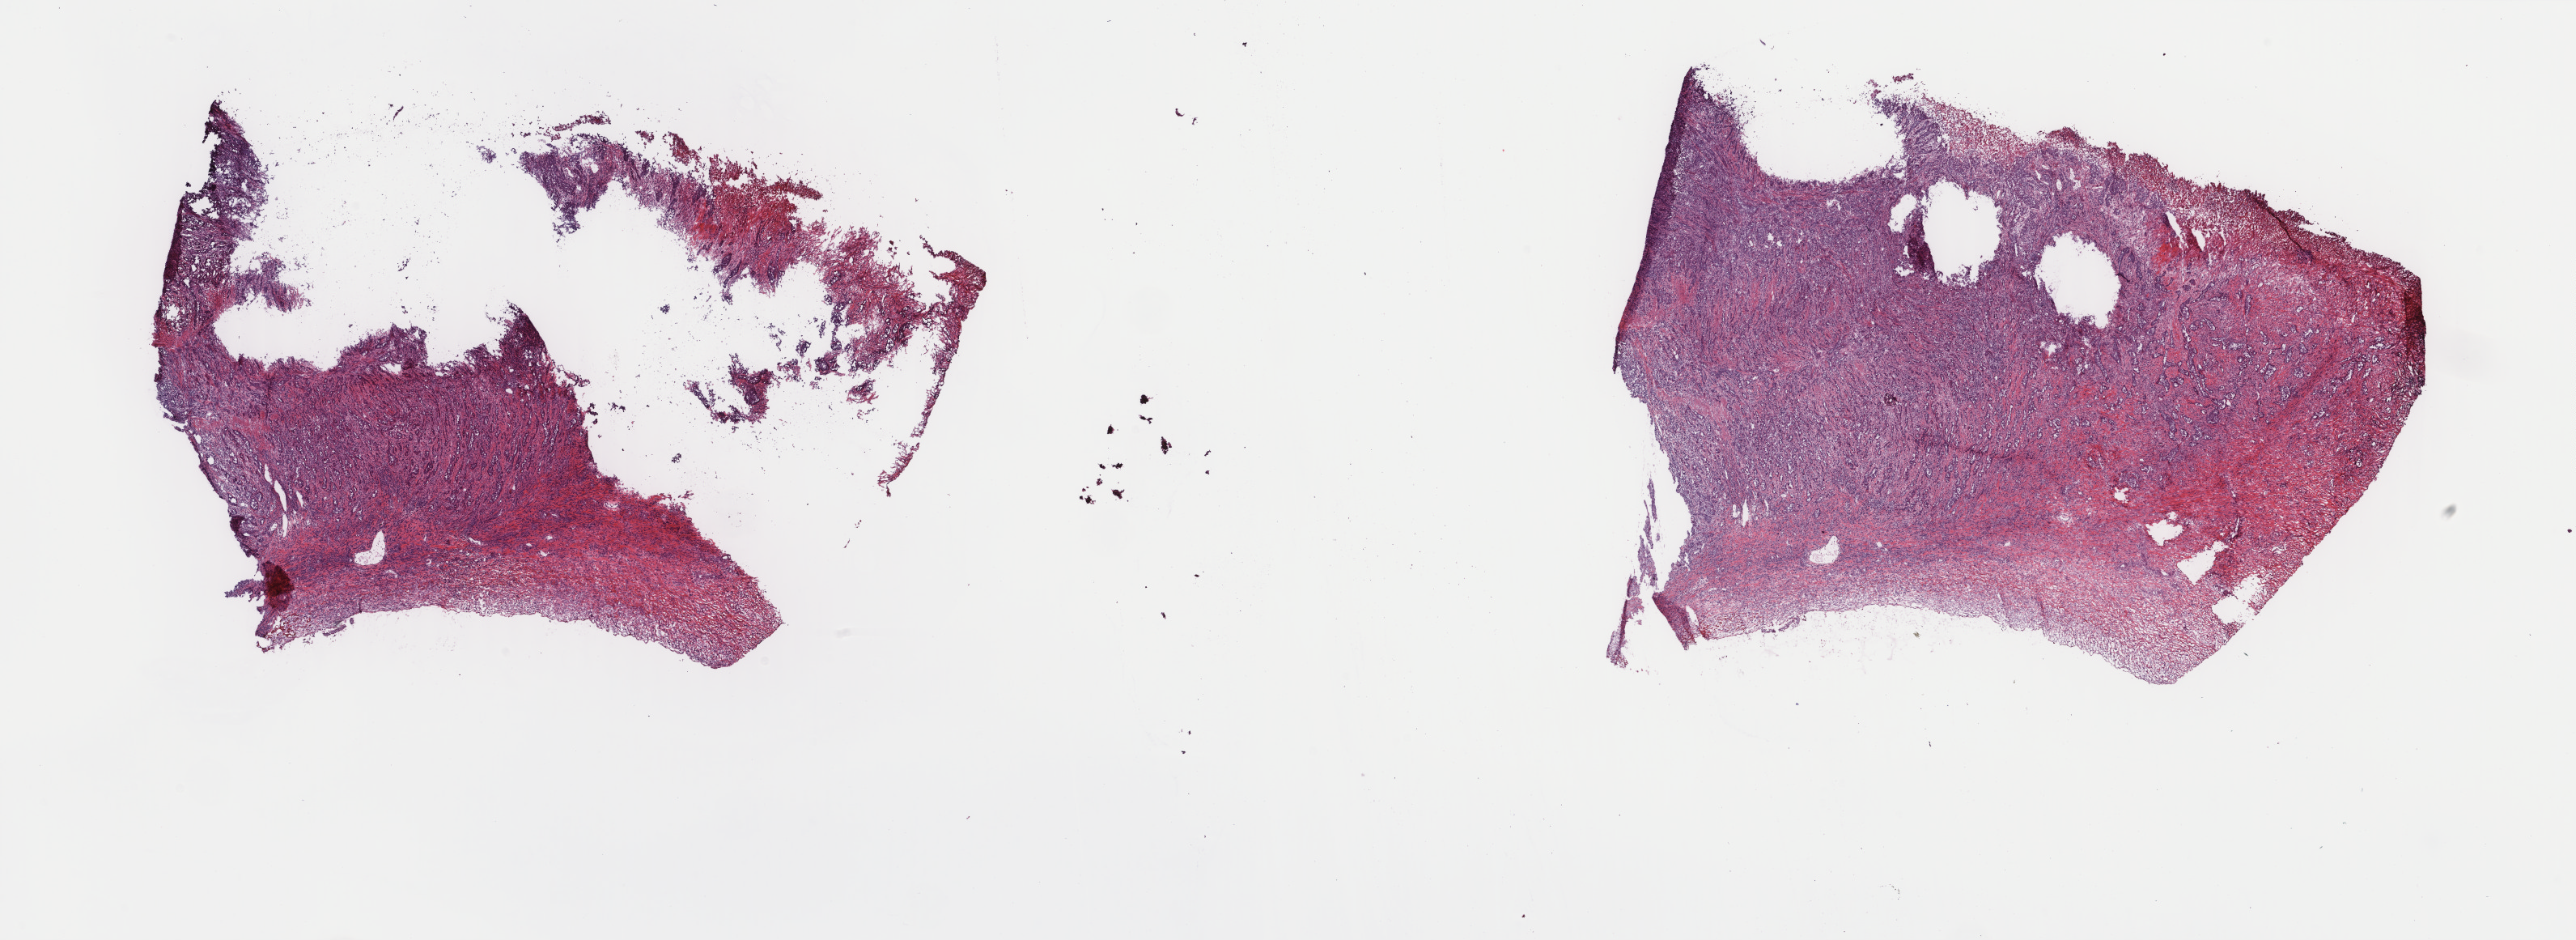
Whole-slide histology image, H&E, low-resolution overview of the scanned area, about 25.3 x 9.2 mm (from a 40x scan); frozen section from the top of the tissue portion; stomach, primary tumour sample. Male patient; age at initial diagnosis 58 years. Composition of this section per pathologist review: tumour cells 80%, tumour nuclei 90%.
Pathologic diagnosis: Adenocarcinoma, NOS.